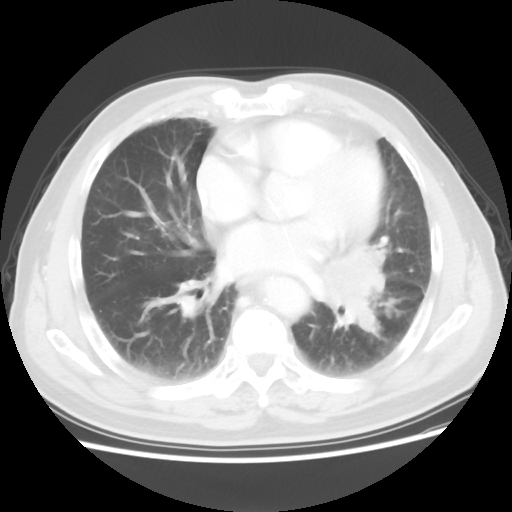
Chest CT, one axial slice. Slice 27 of 56 in the series (ordered by position). Reconstruction kernel STANDARD. 120 kVp. Lung window (W 1500 / L -600 HU). 5 mm slice thickness. 512 × 512 image matrix, field of view 360 × 360 mm. Patient: male, 75 years. From the clinical record (not read from this slice): clinical TNM (as recorded): T3 N0 M0.
Annotated regions visible in this slice (rectangle marked by the reading radiologist):
- lung tumour (recorded histology: squamous cell carcinoma): bounding box [x1, y1, x2, y2] px = [313, 240, 394, 333]